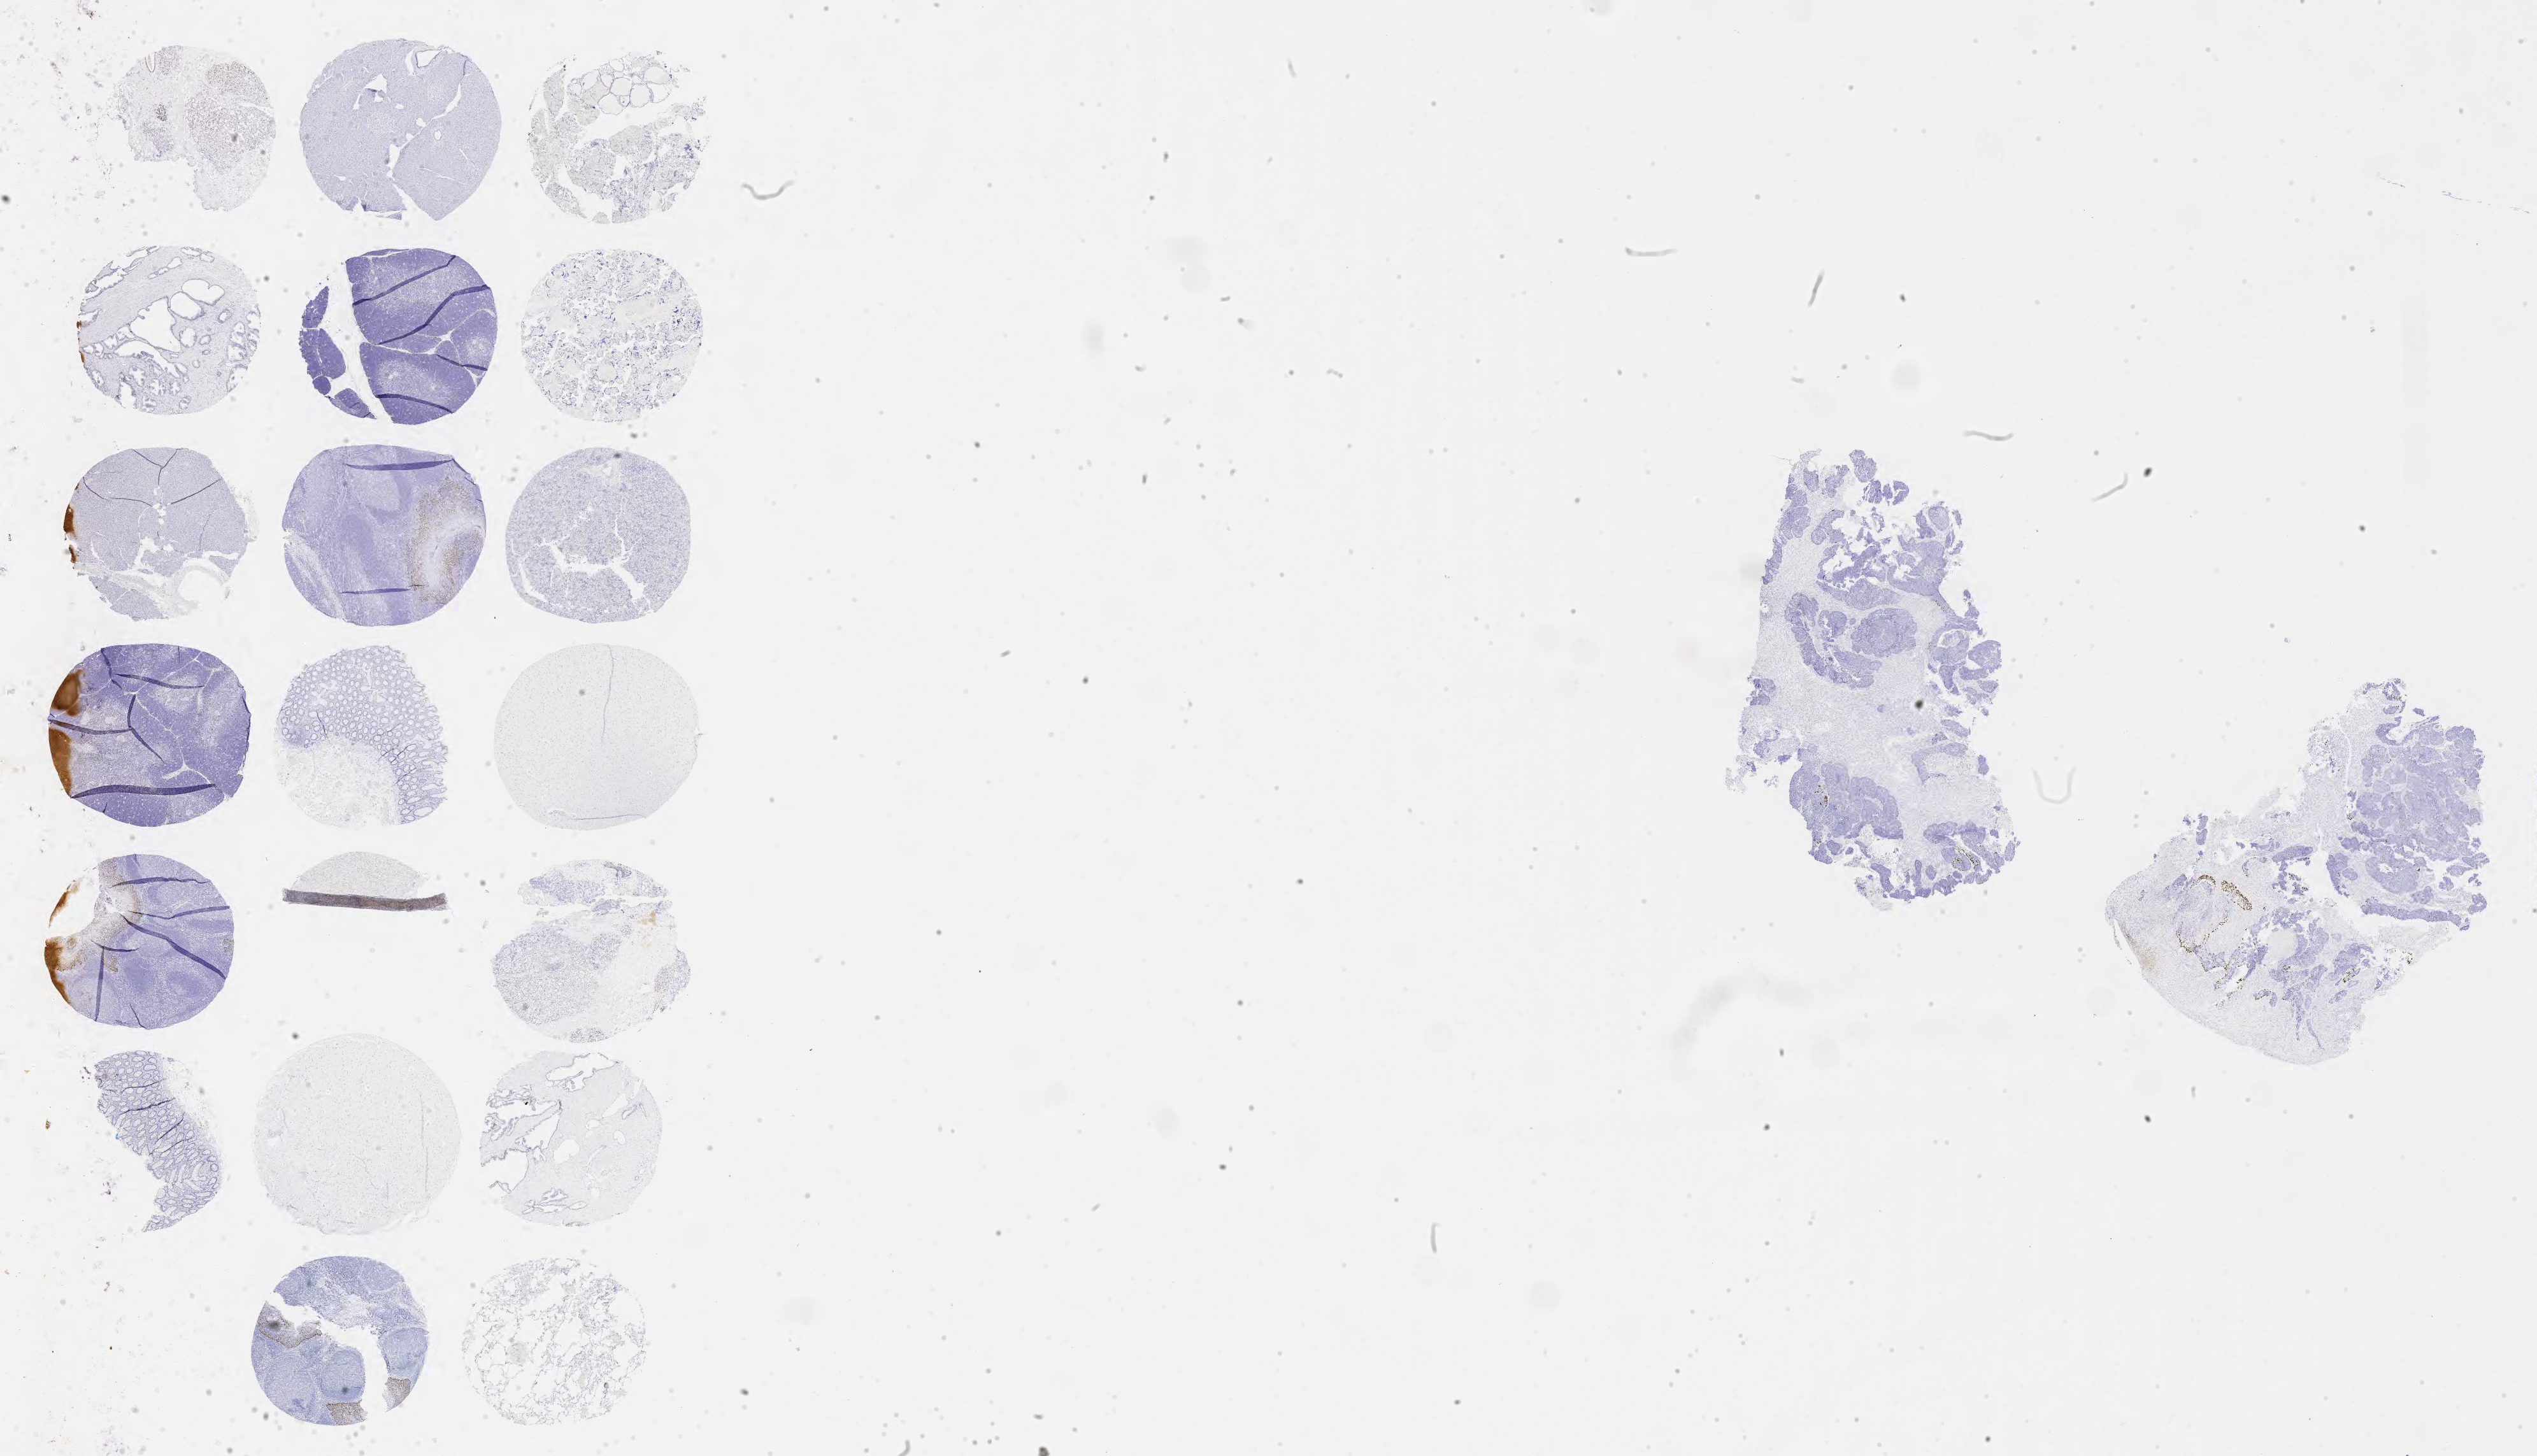
IHC for p40, whole-slide image — shown as a low-resolution overview of the whole scanned area (about 32.2 x 18.5 mm). Specimen: tumor tissue. Anatomic site: cervix. Patient female; 38 years old.
Histologic diagnosis: Squamous cell carcinoma, large cell, nonkeratinizing, NOS.